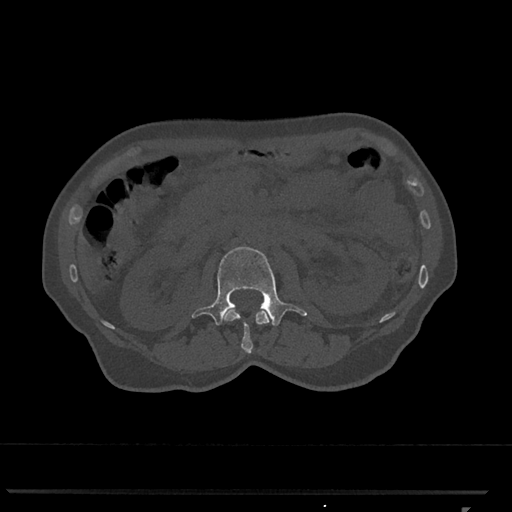
CT including the spine, one axial slice; position 358 of 793 along the scan axis; reconstruction kernel Br40s/3; 120 kVp; bone window (W 1800 / L 400 HU); 0.5 mm slice thickness; 512 × 512 image matrix, field of view 380 × 380 mm. Female patient, age 62 years. Case-level facts recorded for this patient, not image findings: primary cancer: renal.
Structures marked on this image (semi-automatically segmented with operator editing):
- L1 vertebra: box from (x=224, y=309) to (x=272, y=354) px
- L2 vertebra: (x=192, y=247)–(x=307, y=326)